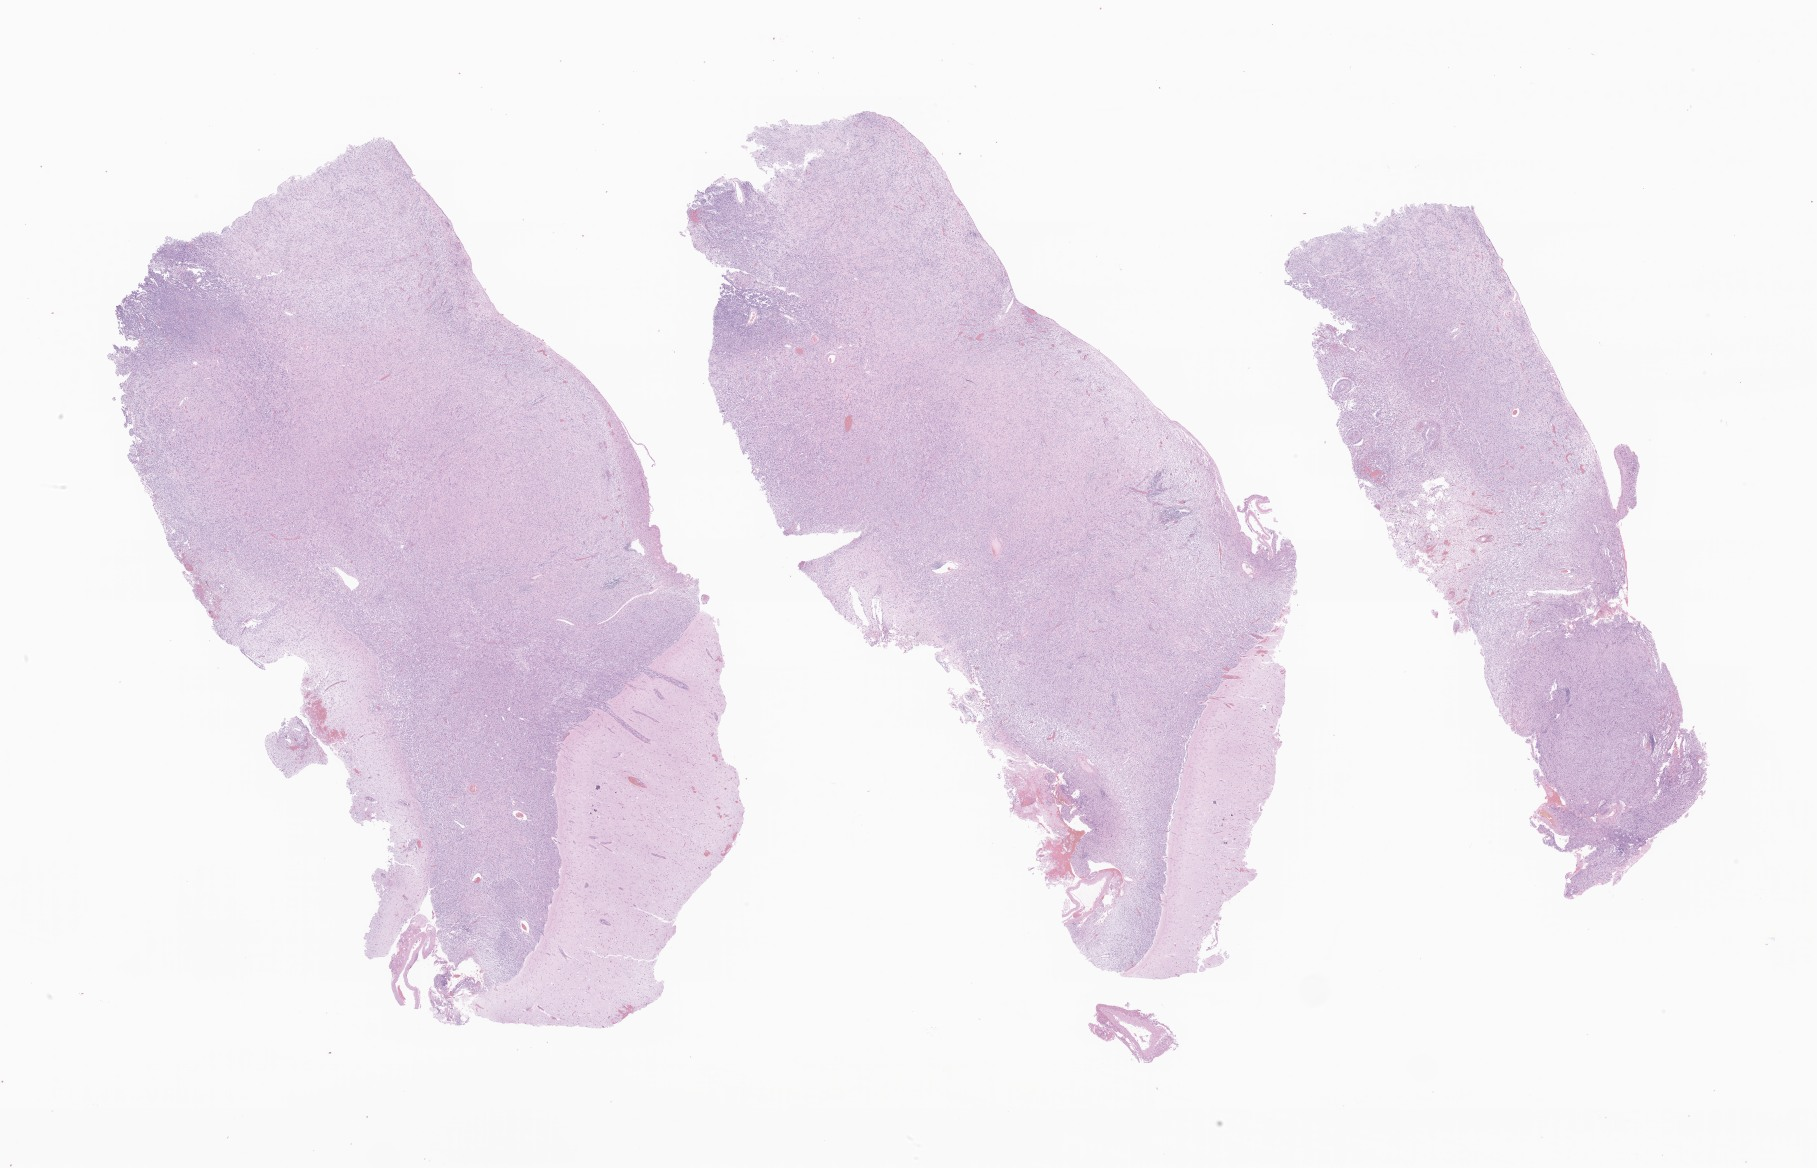
Whole-slide image, hematoxylin and eosin (H&E) stain of tumor tissue from the frontal lobe — shown as a low-resolution overview of the whole scanned area (about 30.7 x 19.7 mm). Formalin-fixed paraffin-embedded section. Patient: female, age 100 months (8 years 4 months).
Diagnosis (ICD-O-3 morphology term): Pleomorphic xanthoastrocytoma, NOS.